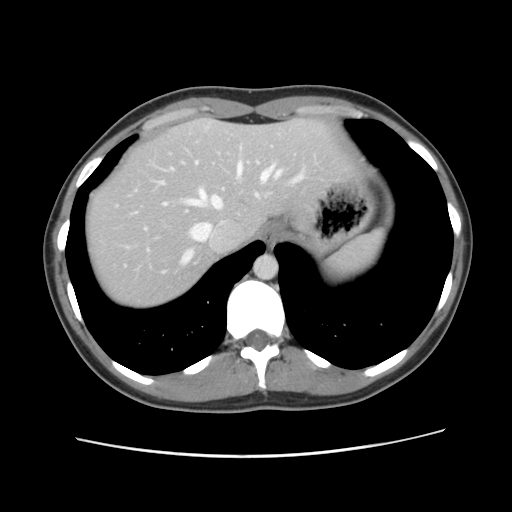
Contrast-enhanced abdominal CT, one axial slice. 120 kVp. Soft-tissue window (W 400 / L 40 HU). 2.5 mm slice thickness. 512 × 512 image matrix, field of view 339 × 339 mm. Female patient, age 33 years. Case-level facts recorded for this patient, not image findings: diagnosis: colorectal cancer liver metastases, imaged before liver resection; multiple liver metastases: yes.
Annotated regions visible in this slice (expert manual segmentation):
- hepatic veins: box from (x=160, y=161) to (x=305, y=264) px
- liver: (x=85, y=118)–(x=350, y=309)
- planned liver remnant (the part of the liver to remain after resection): (x=85, y=118)–(x=350, y=310)
- portal vein (with intrahepatic branches): (x=115, y=204)–(x=150, y=251)